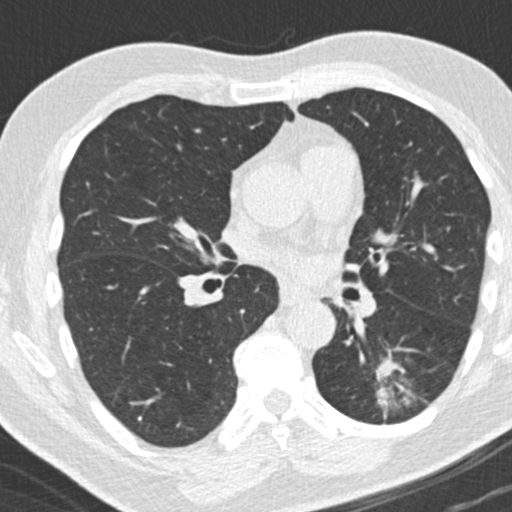
Chest CT (low-dose screening protocol), one axial image. Third screening round (two years after baseline). Lung window (W 1500 / L -600 HU). Standard (soft-tissue) reconstruction kernel (B30f). 512 × 512 image matrix. Male, age 66 years at enrolment.
• Lesion marked by an expert reader, bounding box [x1, y1, x2, y2] px = [357, 355, 425, 427].
• Screening reader's record for this exam (one nodule recorded; not confirmed to be the boxed lesion): non-calcified nodule or mass ≥4 mm, left lower lobe, 31 × 24 mm, spiculated (stellate) margins, pre-existing on the prior screen: yes; interval growth: yes.
• Later outcome: lung cancer diagnosed 56 days after this screen — adenocarcinoma, NOS, left lower lobe, poorly differentiated (G3), stage IB (AJCC 6th edition), 38 mm at pathology.